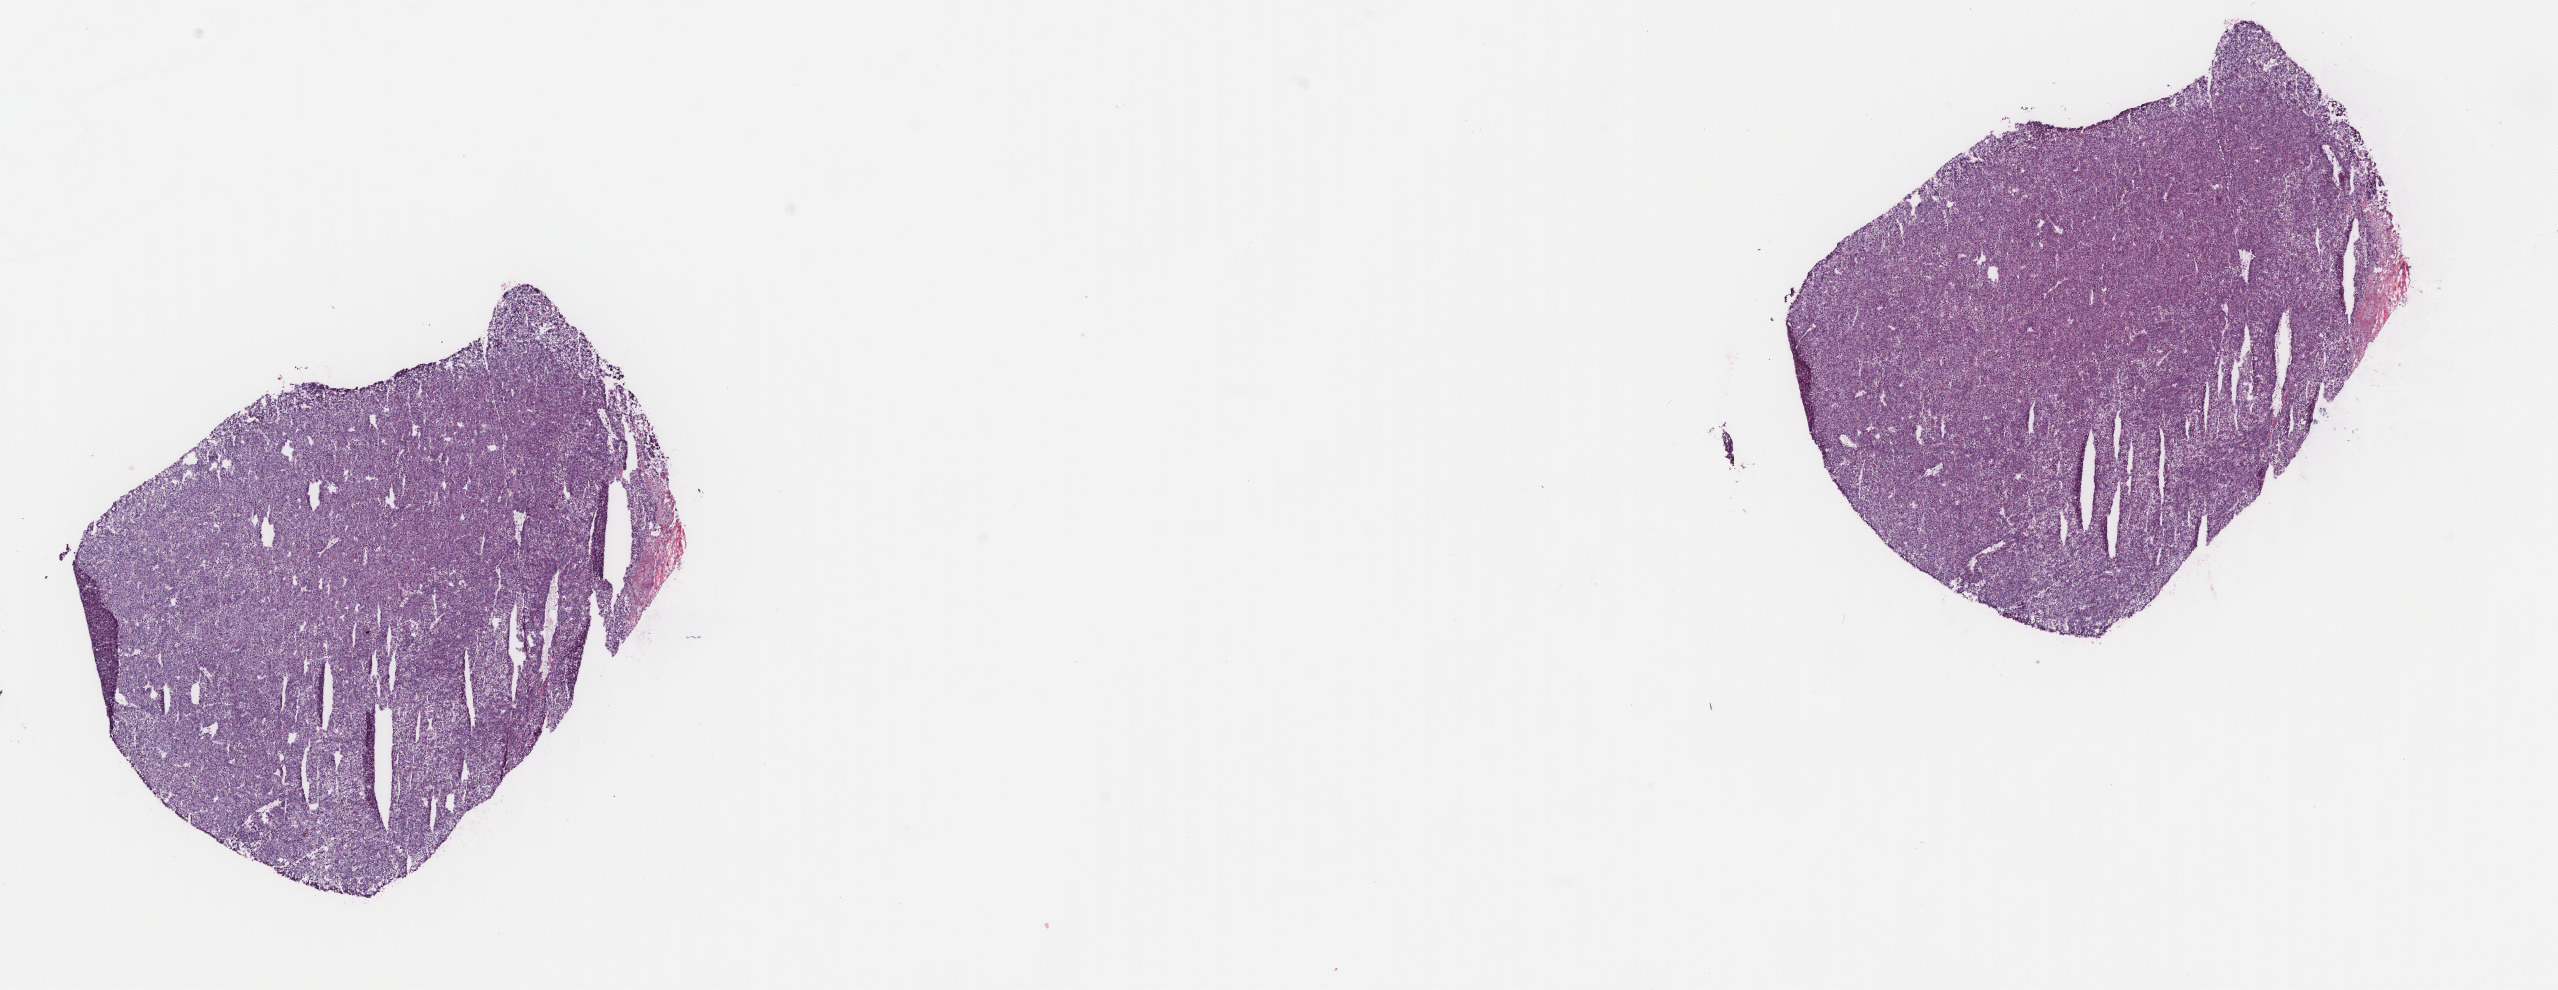
Whole-slide histology image, Hematoxylin and eosin (H&E) stained — whole scanned area (about 20.3 x 7.9 mm) shown as a low-resolution overview, frozen section from the top of the tissue portion, liver, primary tumour sample. Female patient; age at initial diagnosis 46 years. Histologic grade: G2 (moderately differentiated). Pathologist review of this section (percent, as recorded): tumour cells 97%, tumour nuclei 98%, normal cells 0%, stromal cells 3%, necrosis 0%. Infiltration values recorded for this section: lymphocyte infiltration 0%, monocyte infiltration 0%, neutrophil infiltration 0%.
AJCC pathologic stage: I. Pathologic diagnosis: Hepatocellular carcinoma, NOS.